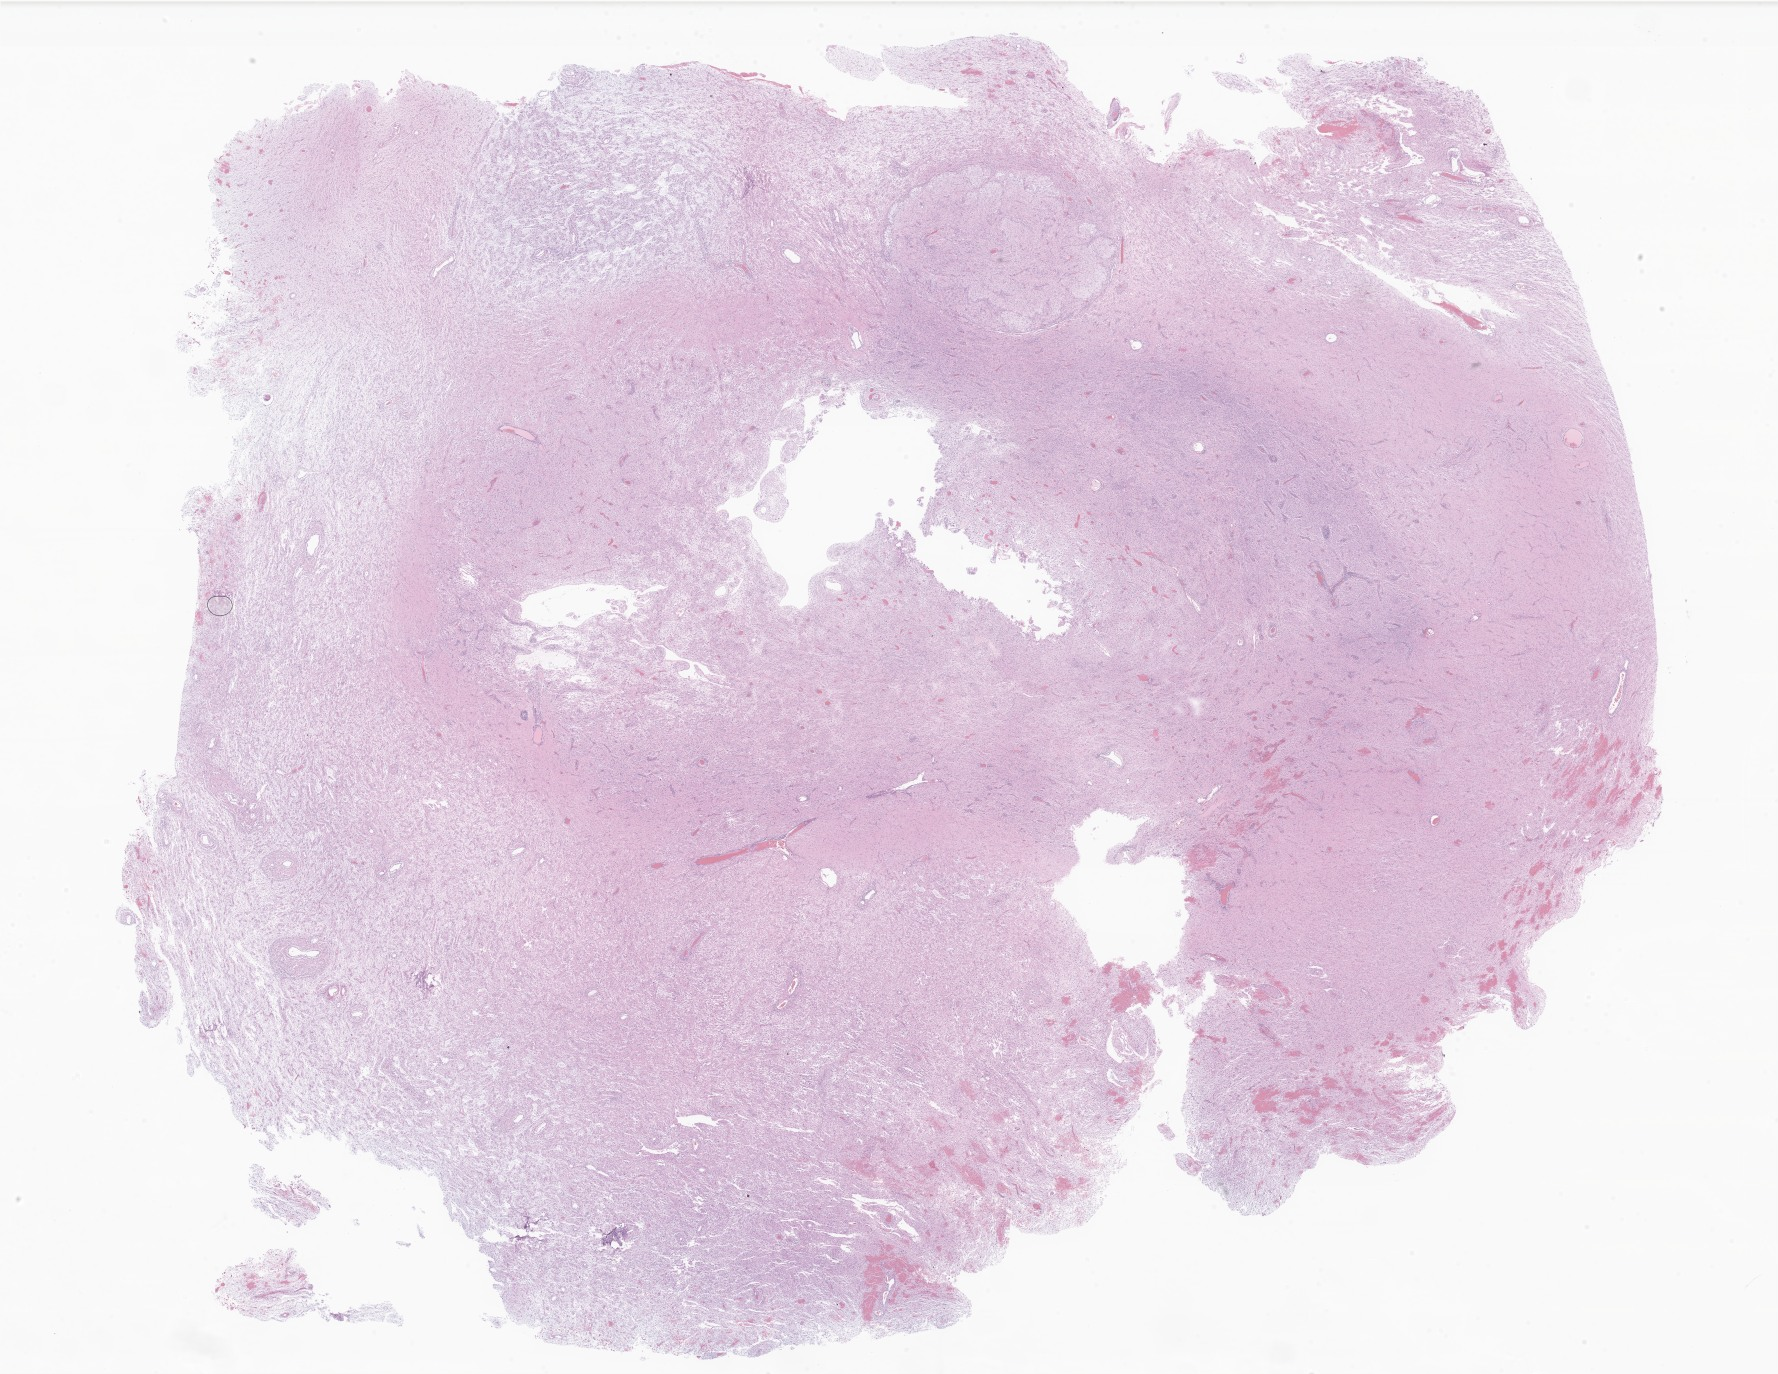
Whole-slide image, haematoxylin and eosin stain of tumor tissue from the brain, low-resolution overview of the scanned area, about 30.0 x 23.2 mm. FFPE section. Patient male; age 184 months.
Recorded diagnosis: Pilocytic astrocytoma.